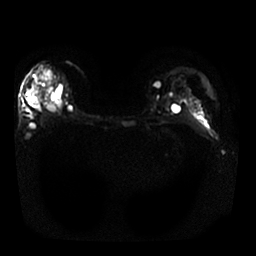
Breast MRI, one axial slice; position 18 of 30 along the scan axis; diffusion-weighted series; image 2 of 4 stored at this slice position (different b-values; order by instance number); 1.5 T; 256 × 256 image matrix, field of view 340 × 340 mm. Female patient.
Structures marked on this image (manually delineated by an expert):
- tumour on diffusion-weighted imaging: bounding box [x1, y1, x2, y2] px = [41, 69, 56, 84]